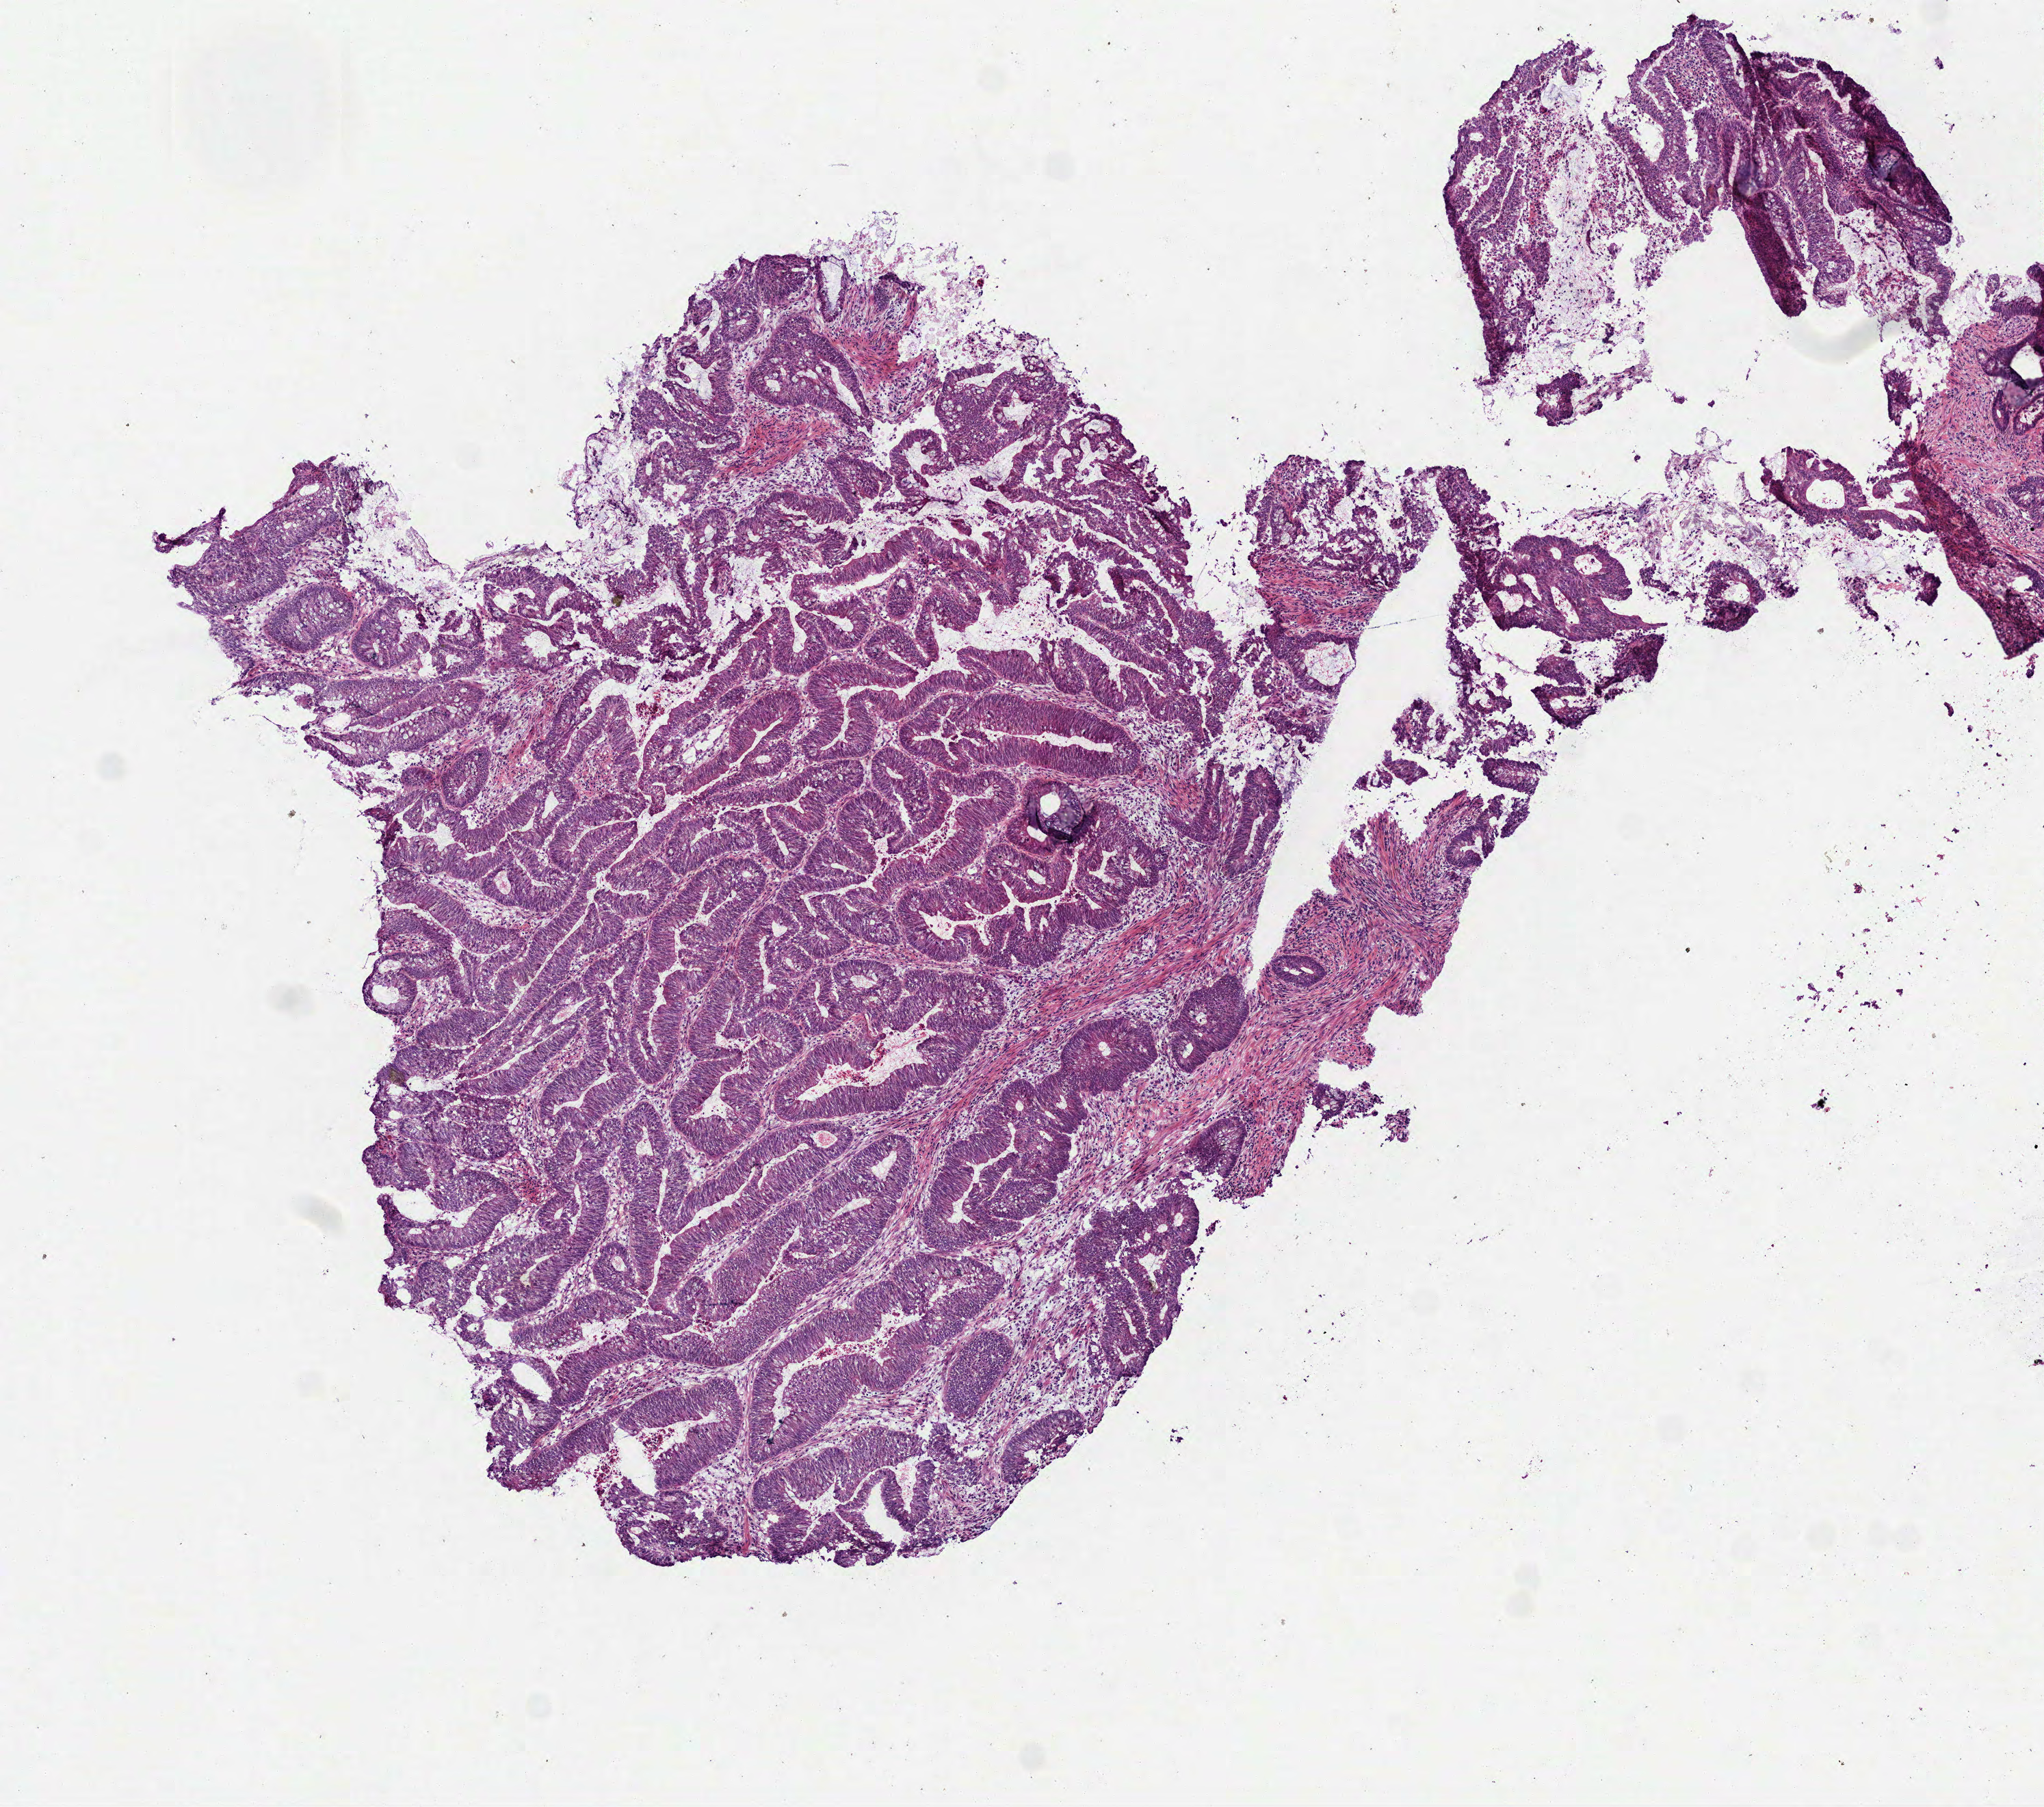
Whole-slide histology image, Hematoxylin and eosin (H&E) stained, low-resolution overview of the scanned area, about 6.0 x 5.3 mm, frozen section from the bottom of the tissue portion, primary tumour sample from the colon. Female patient. Pathologist review of this section (percent, as recorded): tumour cells 82%, tumour nuclei 75%, normal cells 0%, stromal cells 18%, necrosis 0%.
AJCC pathologic stage: IIA (6th edition). Diagnosis: Adenocarcinoma, NOS (cecum).